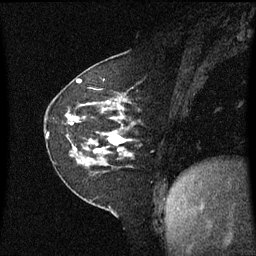
Breast MRI (dynamic contrast-enhanced), one sagittal slice. Position 22 of 60 along the scan axis. Dynamic contrast-enhanced series, image 2 of 3 at this slice position (ordered by acquisition). 1.5 T. TE 4.2 ms, TR 8.4 ms. 2 mm slice thickness. 256 × 256 image matrix, field of view 210 × 210 mm. Patient: female, 60 years. From the clinical record (not read from this slice): setting: breast cancer imaged before/during neoadjuvant chemotherapy; receptor status: triple-negative.
Structures marked on this image (semi-automatically segmented with operator editing):
- analysis volume of interest (the breast-tissue region the enhancement analysis was run in; not a lesion): bounding box (x1, y1, x2, y2) in pixels: (46, 99, 137, 182)
- tumour enhancement mask (voxels above the 70 % enhancement threshold inside the analysis volume of interest): (75, 108, 125, 155)